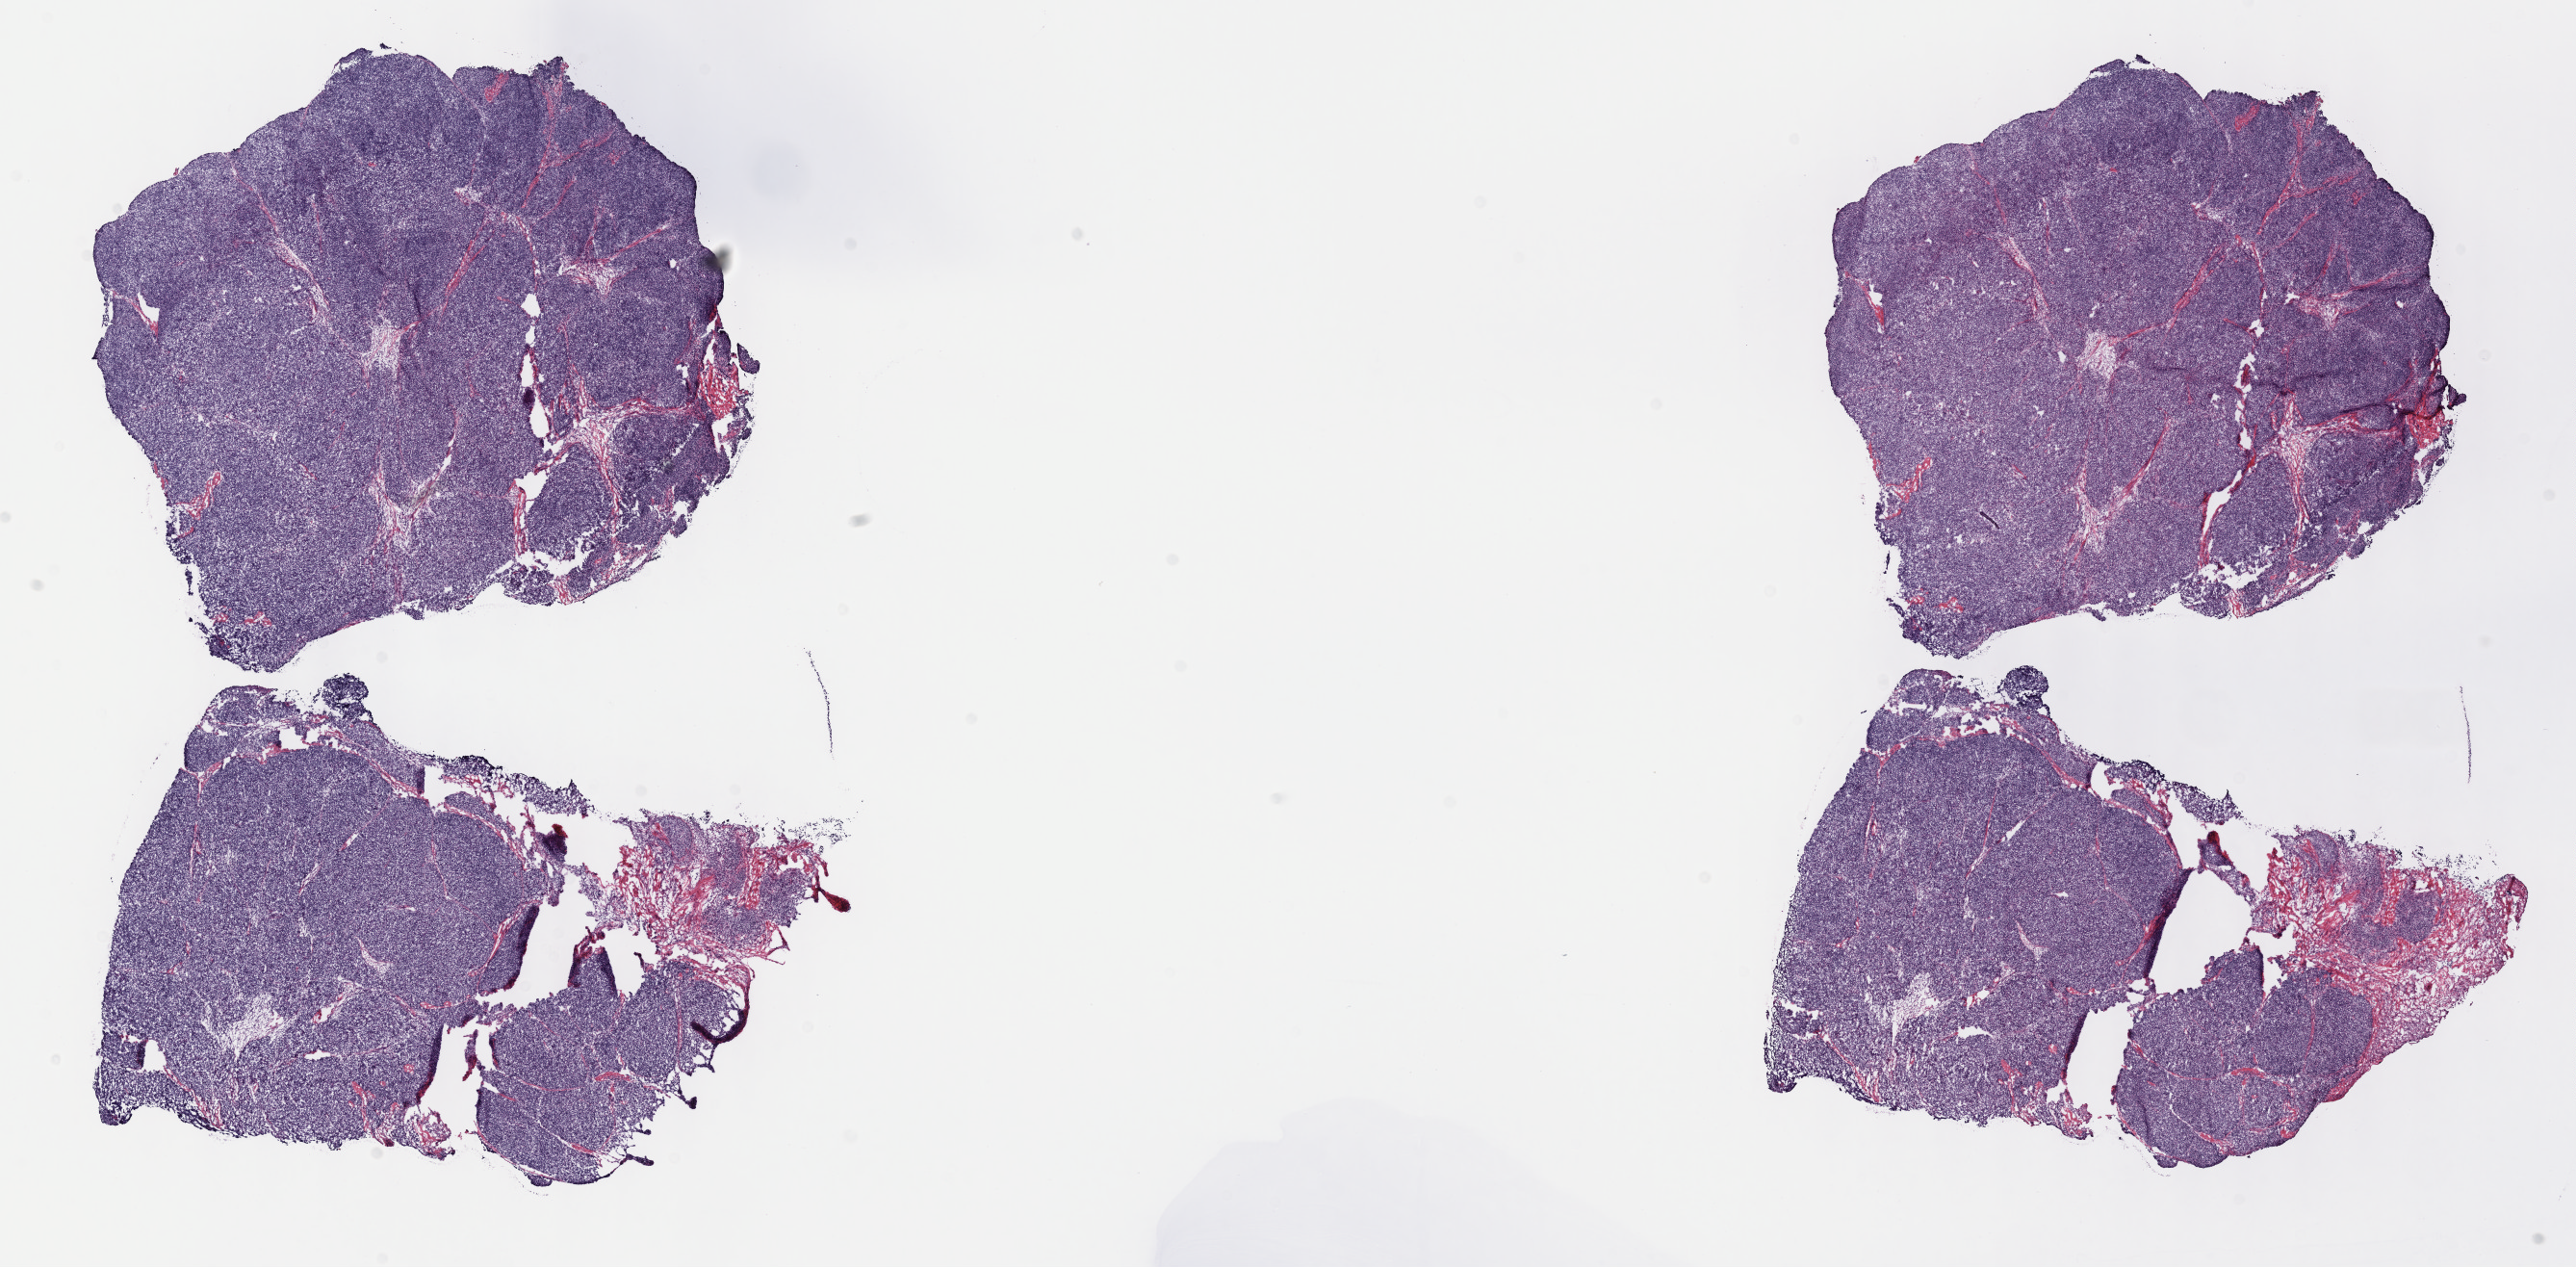
Digitized H&E-stained tissue section (whole slide), a low-resolution overview of the entire scanned area, about 21.6 x 10.6 mm (acquisition: 40x scan), frozen section from the top of the tissue portion, thymus, primary tumour sample. Female, age 61 years at initial diagnosis. Pathologist review of this section (percent, as recorded): tumour cells 85%, tumour nuclei 85%, normal cells 0%, stromal cells 15%, necrosis 0%. Inflammatory infiltration, as recorded: lymphocyte infiltration 2%, monocyte infiltration 1%, neutrophil infiltration 1%.
Histologic diagnosis: Thymoma, type AB, malignant.